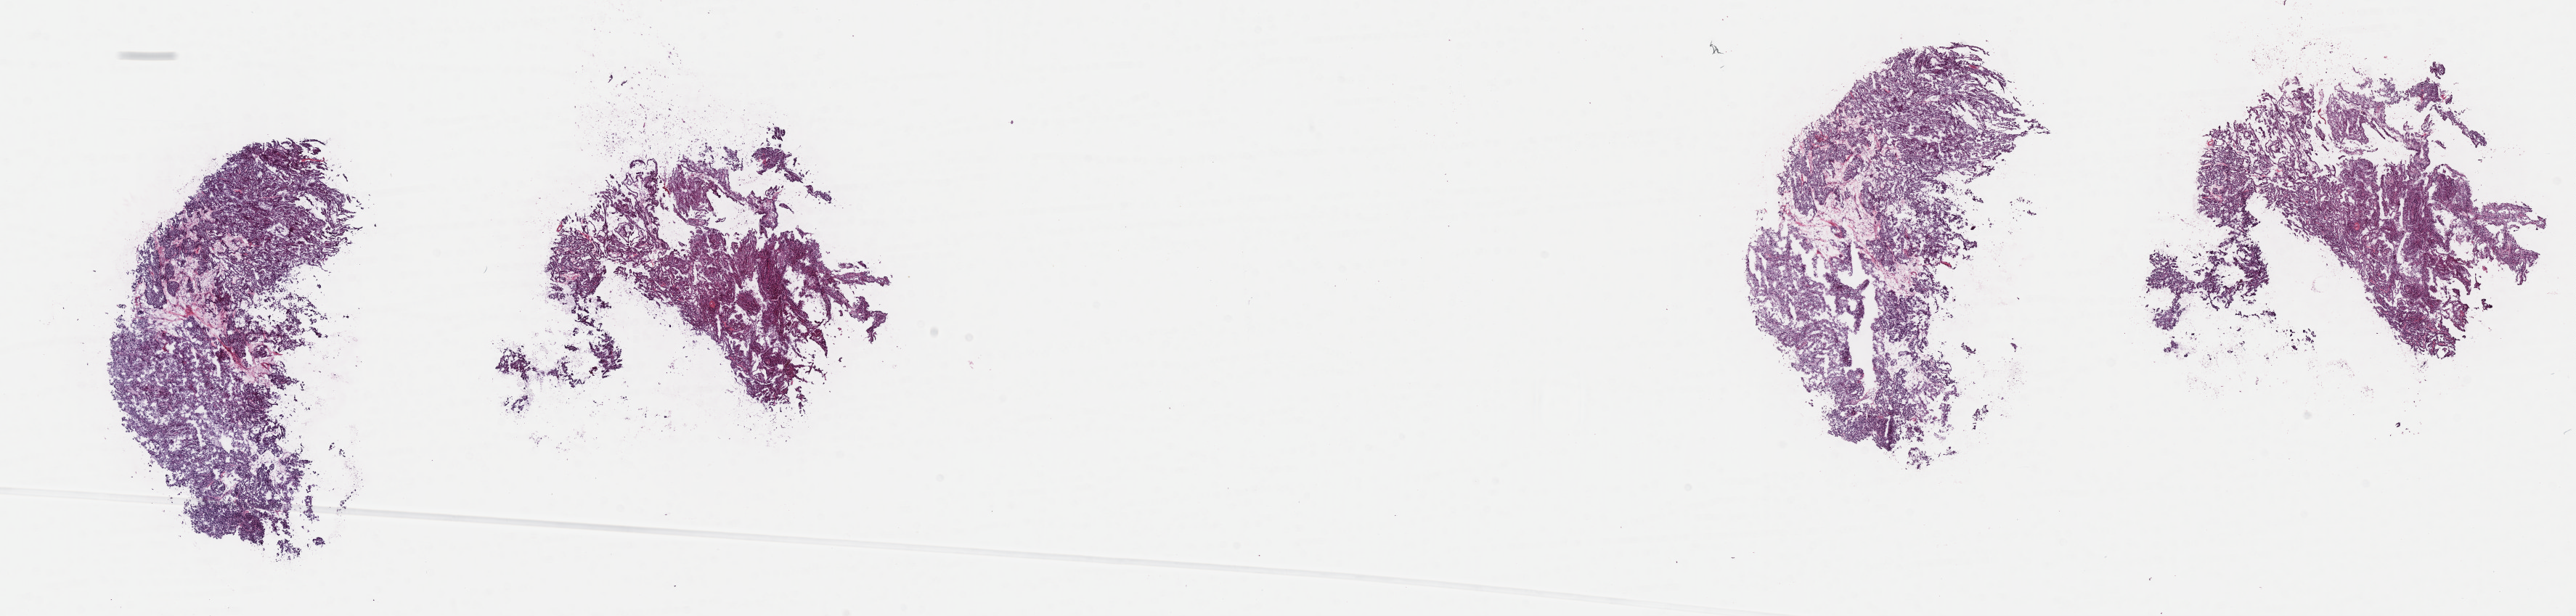
H&E-stained whole-slide image, shown as a low-resolution overview of the whole scanned area (about 28.7 x 6.9 mm); frozen section; kidney, primary tumour sample. Male, age 79 years at initial diagnosis. Pathologist review of this section (percent, as recorded): tumour cells 100%, tumour nuclei 70%.
Histologic diagnosis: Papillary adenocarcinoma, NOS.